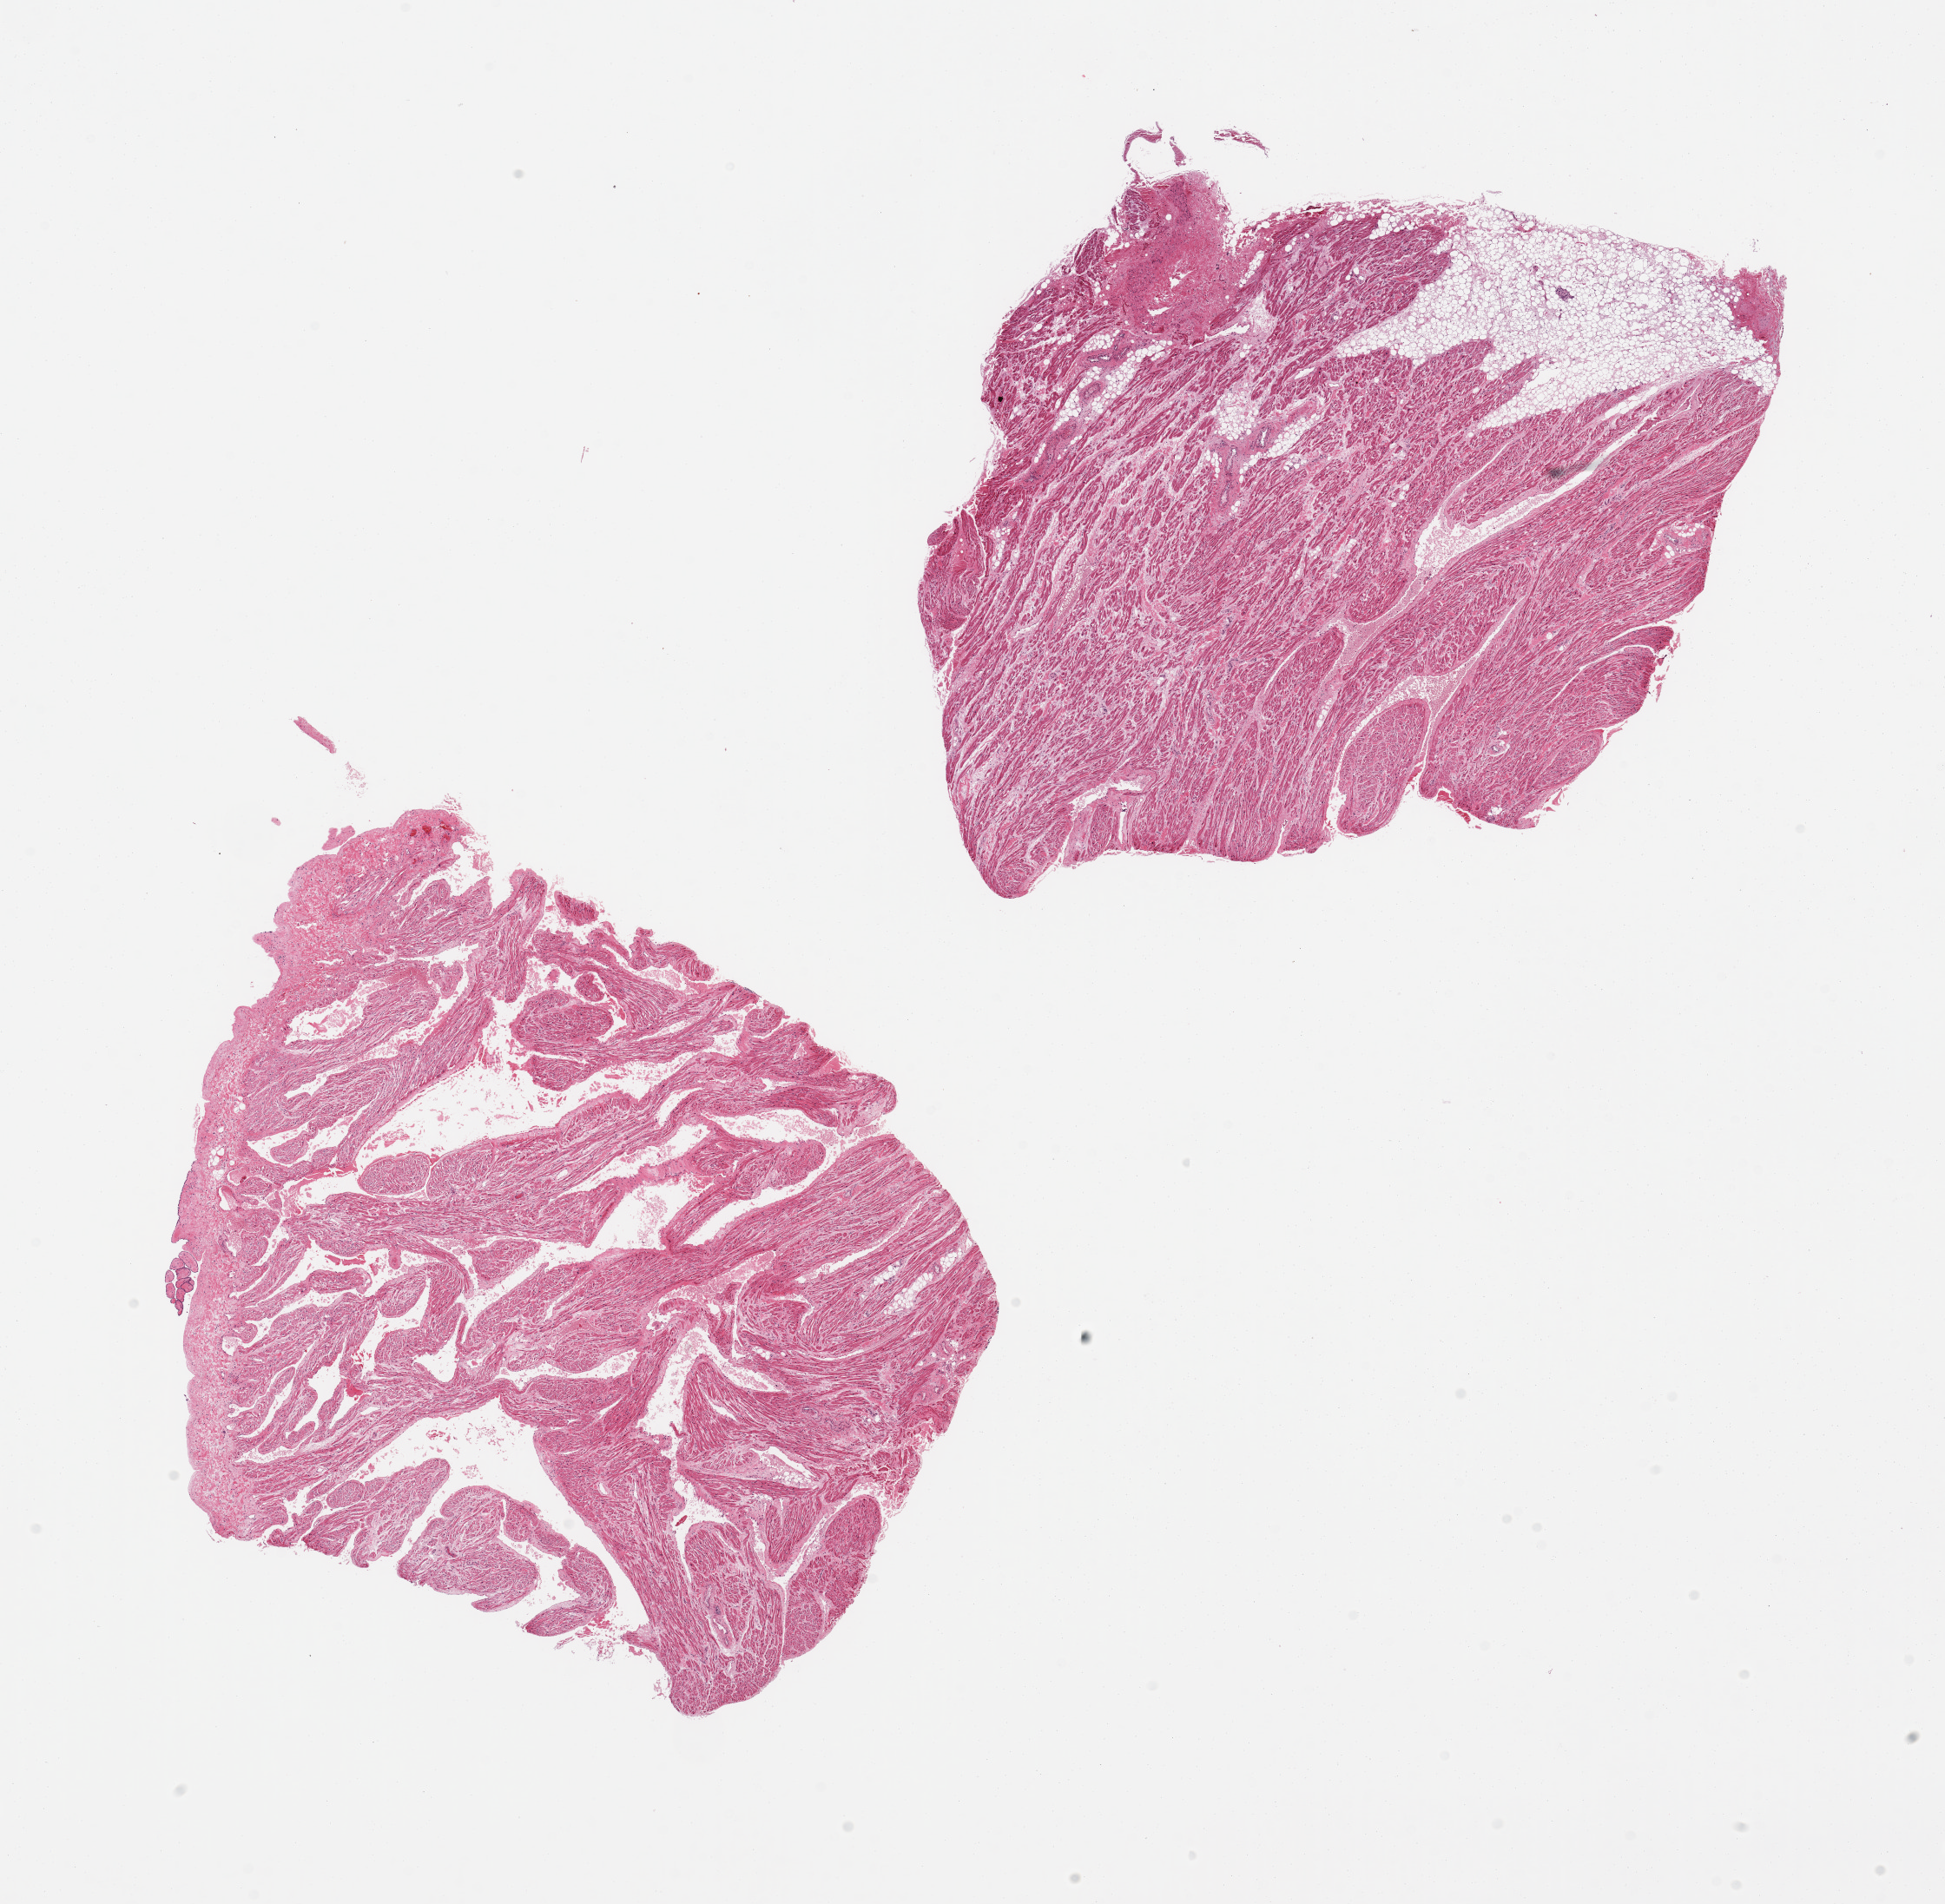
Whole-slide image, hematoxylin and eosin (H&E) stain — whole scanned area (about 17.7 x 17.3 mm, slide scanned at 20x) shown as a low-resolution overview. PAXgene-fixed, paraffin-embedded tissue. Target tissue: auricular appendage. Tissue donor sample. Donor: female.
- review note (as recorded): 2 pieces, no abnormalities